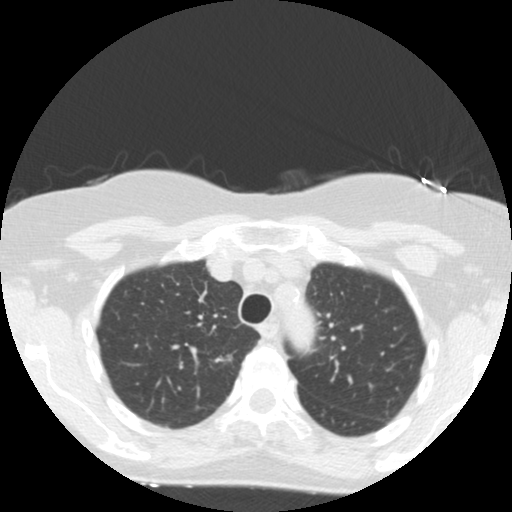
Chest CT (low-dose screening protocol), one axial image; first (baseline) screen; lung window (W 1500 / L -600 HU); slice 37 of 155 in the series; 512 × 512 image matrix, field of view 300 × 300 mm. Female, age 67 years at enrolment. Former smoker at enrolment.
Expert reader's lesion annotation, bounding box [x1, y1, x2, y2] px = [194, 340, 255, 386]. The exam's reader record, not a measurement of the box and not confirmed to be the same lesion: non-calcified nodule or mass ≥4 mm, right upper lobe, 16 × 7 mm, poorly defined margins, mixed attenuation. Official screen result: positive, change unspecified: nodule(s) >= 4 mm or enlarging nodule(s), mass(es), or other non-specific abnormalities suspicious for lung cancer. Participant outcome: lung cancer diagnosed 132 days after this screen — adenocarcinoma, NOS, right upper lobe, moderately differentiated (G2), stage IA (AJCC 6th edition), 13 mm at pathology.